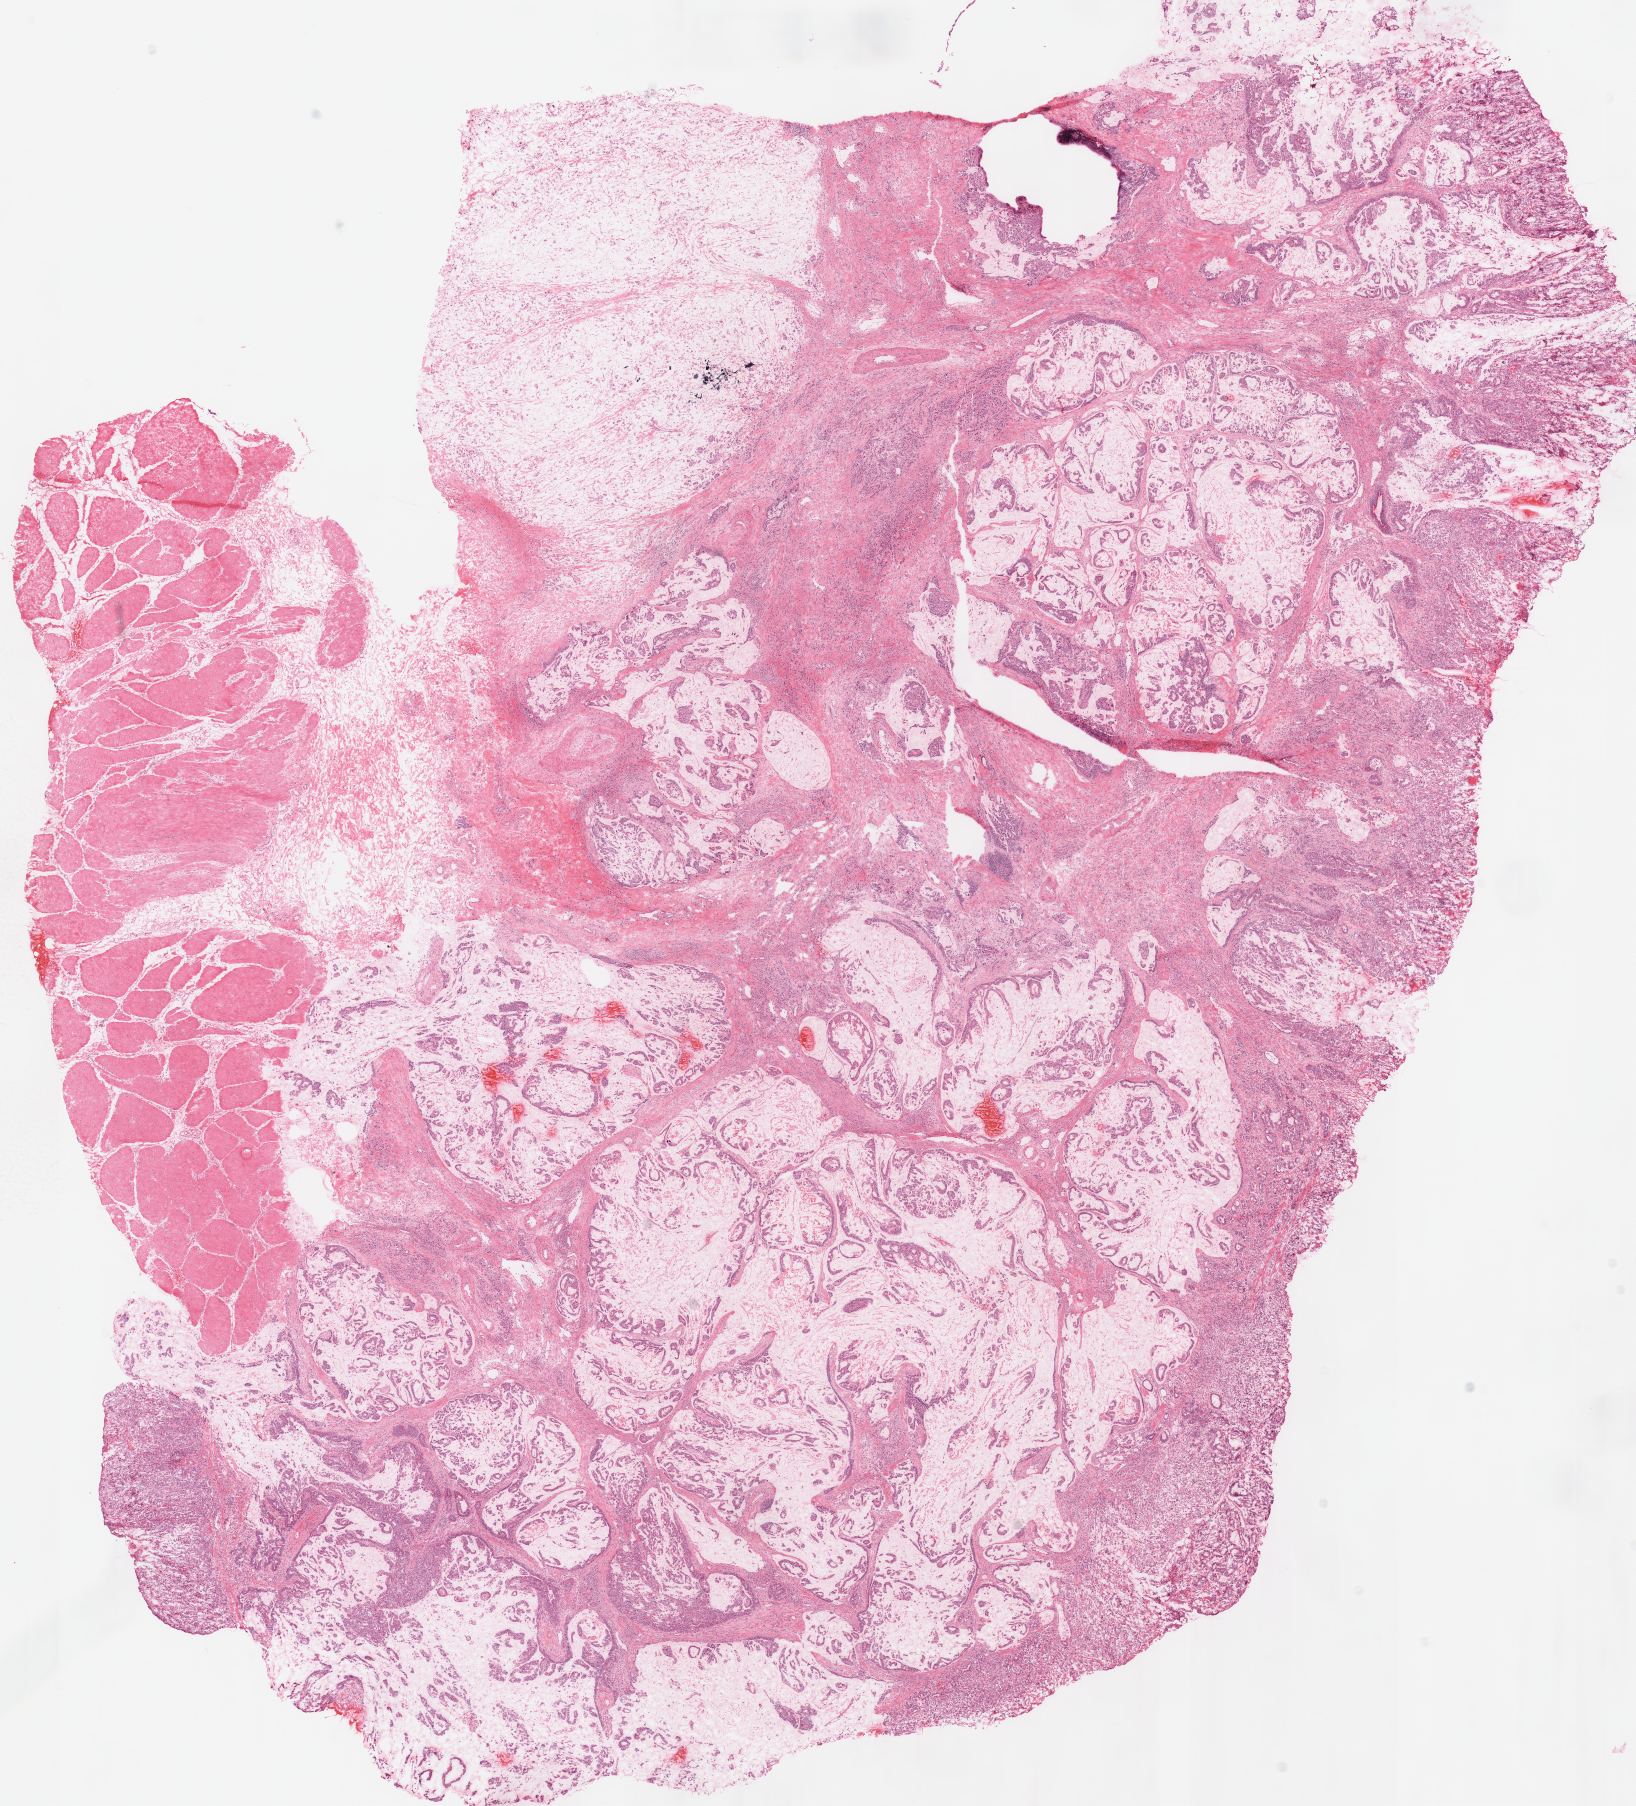
Whole-slide histology image, Hematoxylin and eosin (H&E) stained, shown as a low-resolution overview of the whole scanned area (about 12.9 x 14.2 mm, acquisition: 40x scan). Frozen section. Stomach, primary tumour sample. Female, age 63 years at initial diagnosis.
Diagnosis: Adenocarcinoma, NOS (fundus of stomach).